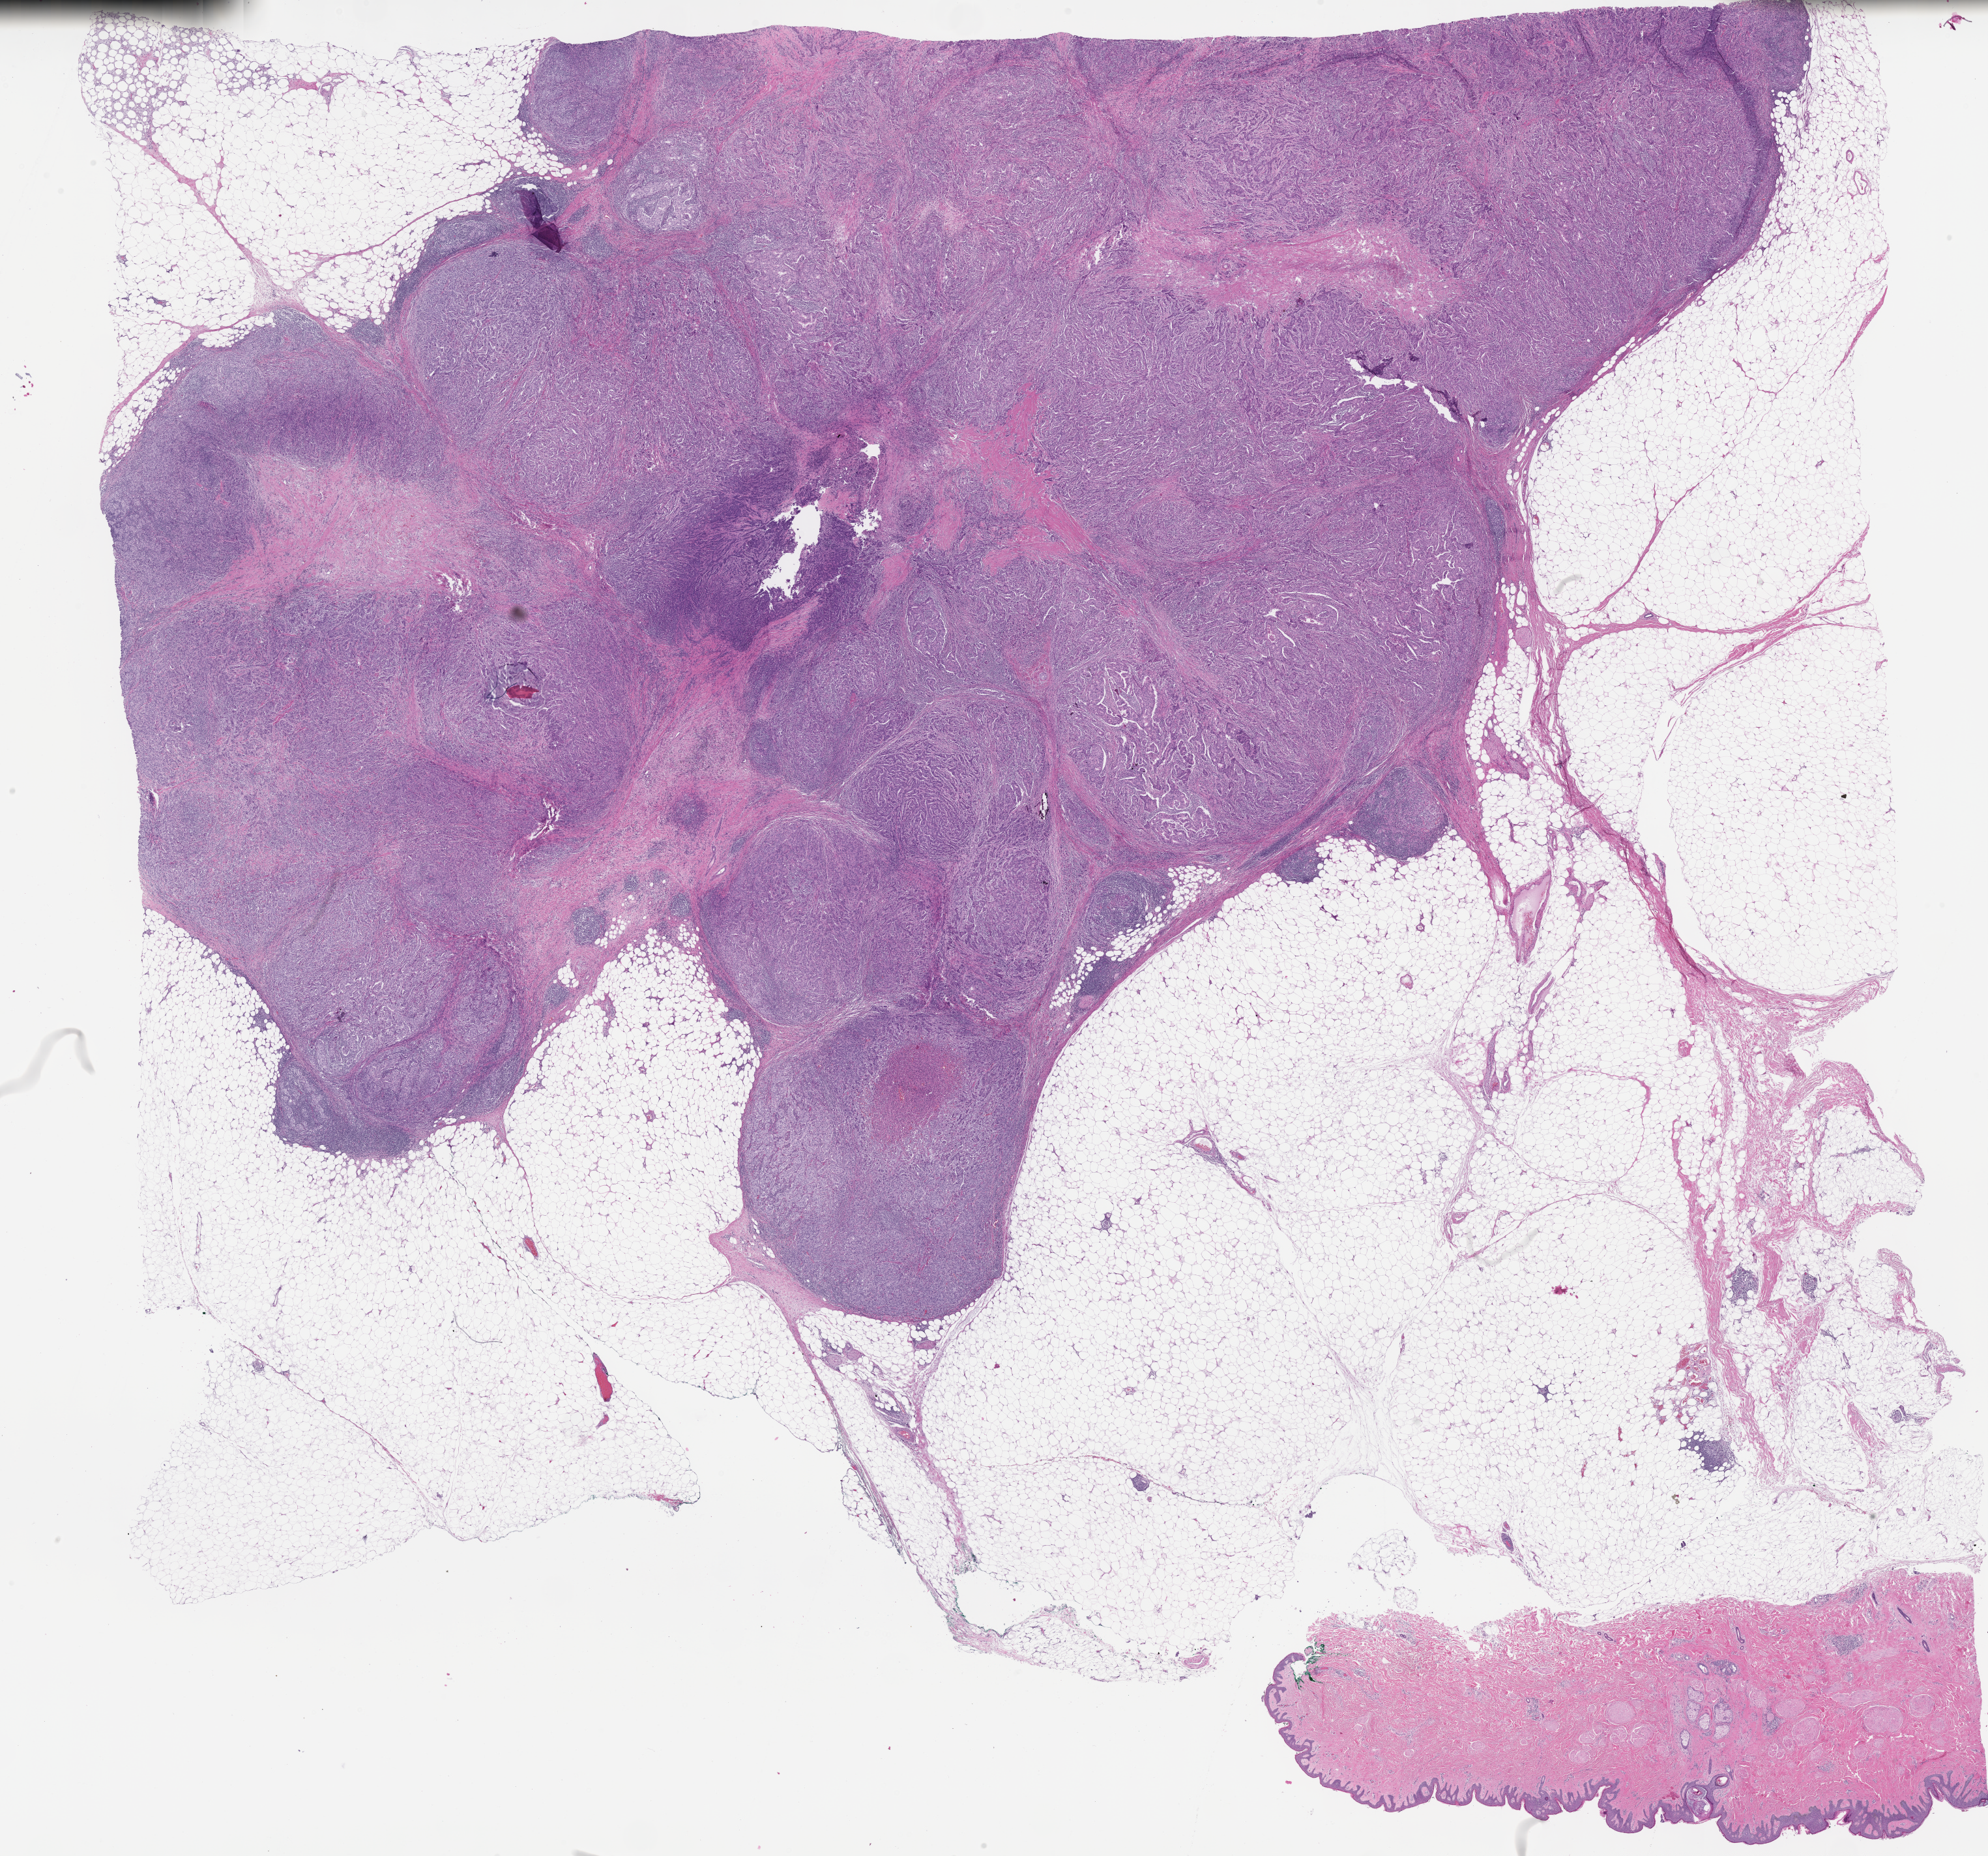
Digitized H&E-stained section — a low-resolution overview of the entire scanned area, about 24.6 x 23.0 mm, formalin-fixed paraffin-embedded section, primary tumor, site: breast. Male, age 79 years at initial diagnosis. Slide review estimates, as recorded: tumor cells 80%, tumor nuclei 80%, stromal cells 17%, necrosis 3%, normal cells 0%. Infiltration values recorded for this section: lymphocyte infiltration 9%, monocyte infiltration 2%, neutrophil infiltration 4%.
Histologic diagnosis: Infiltrating duct carcinoma, NOS.